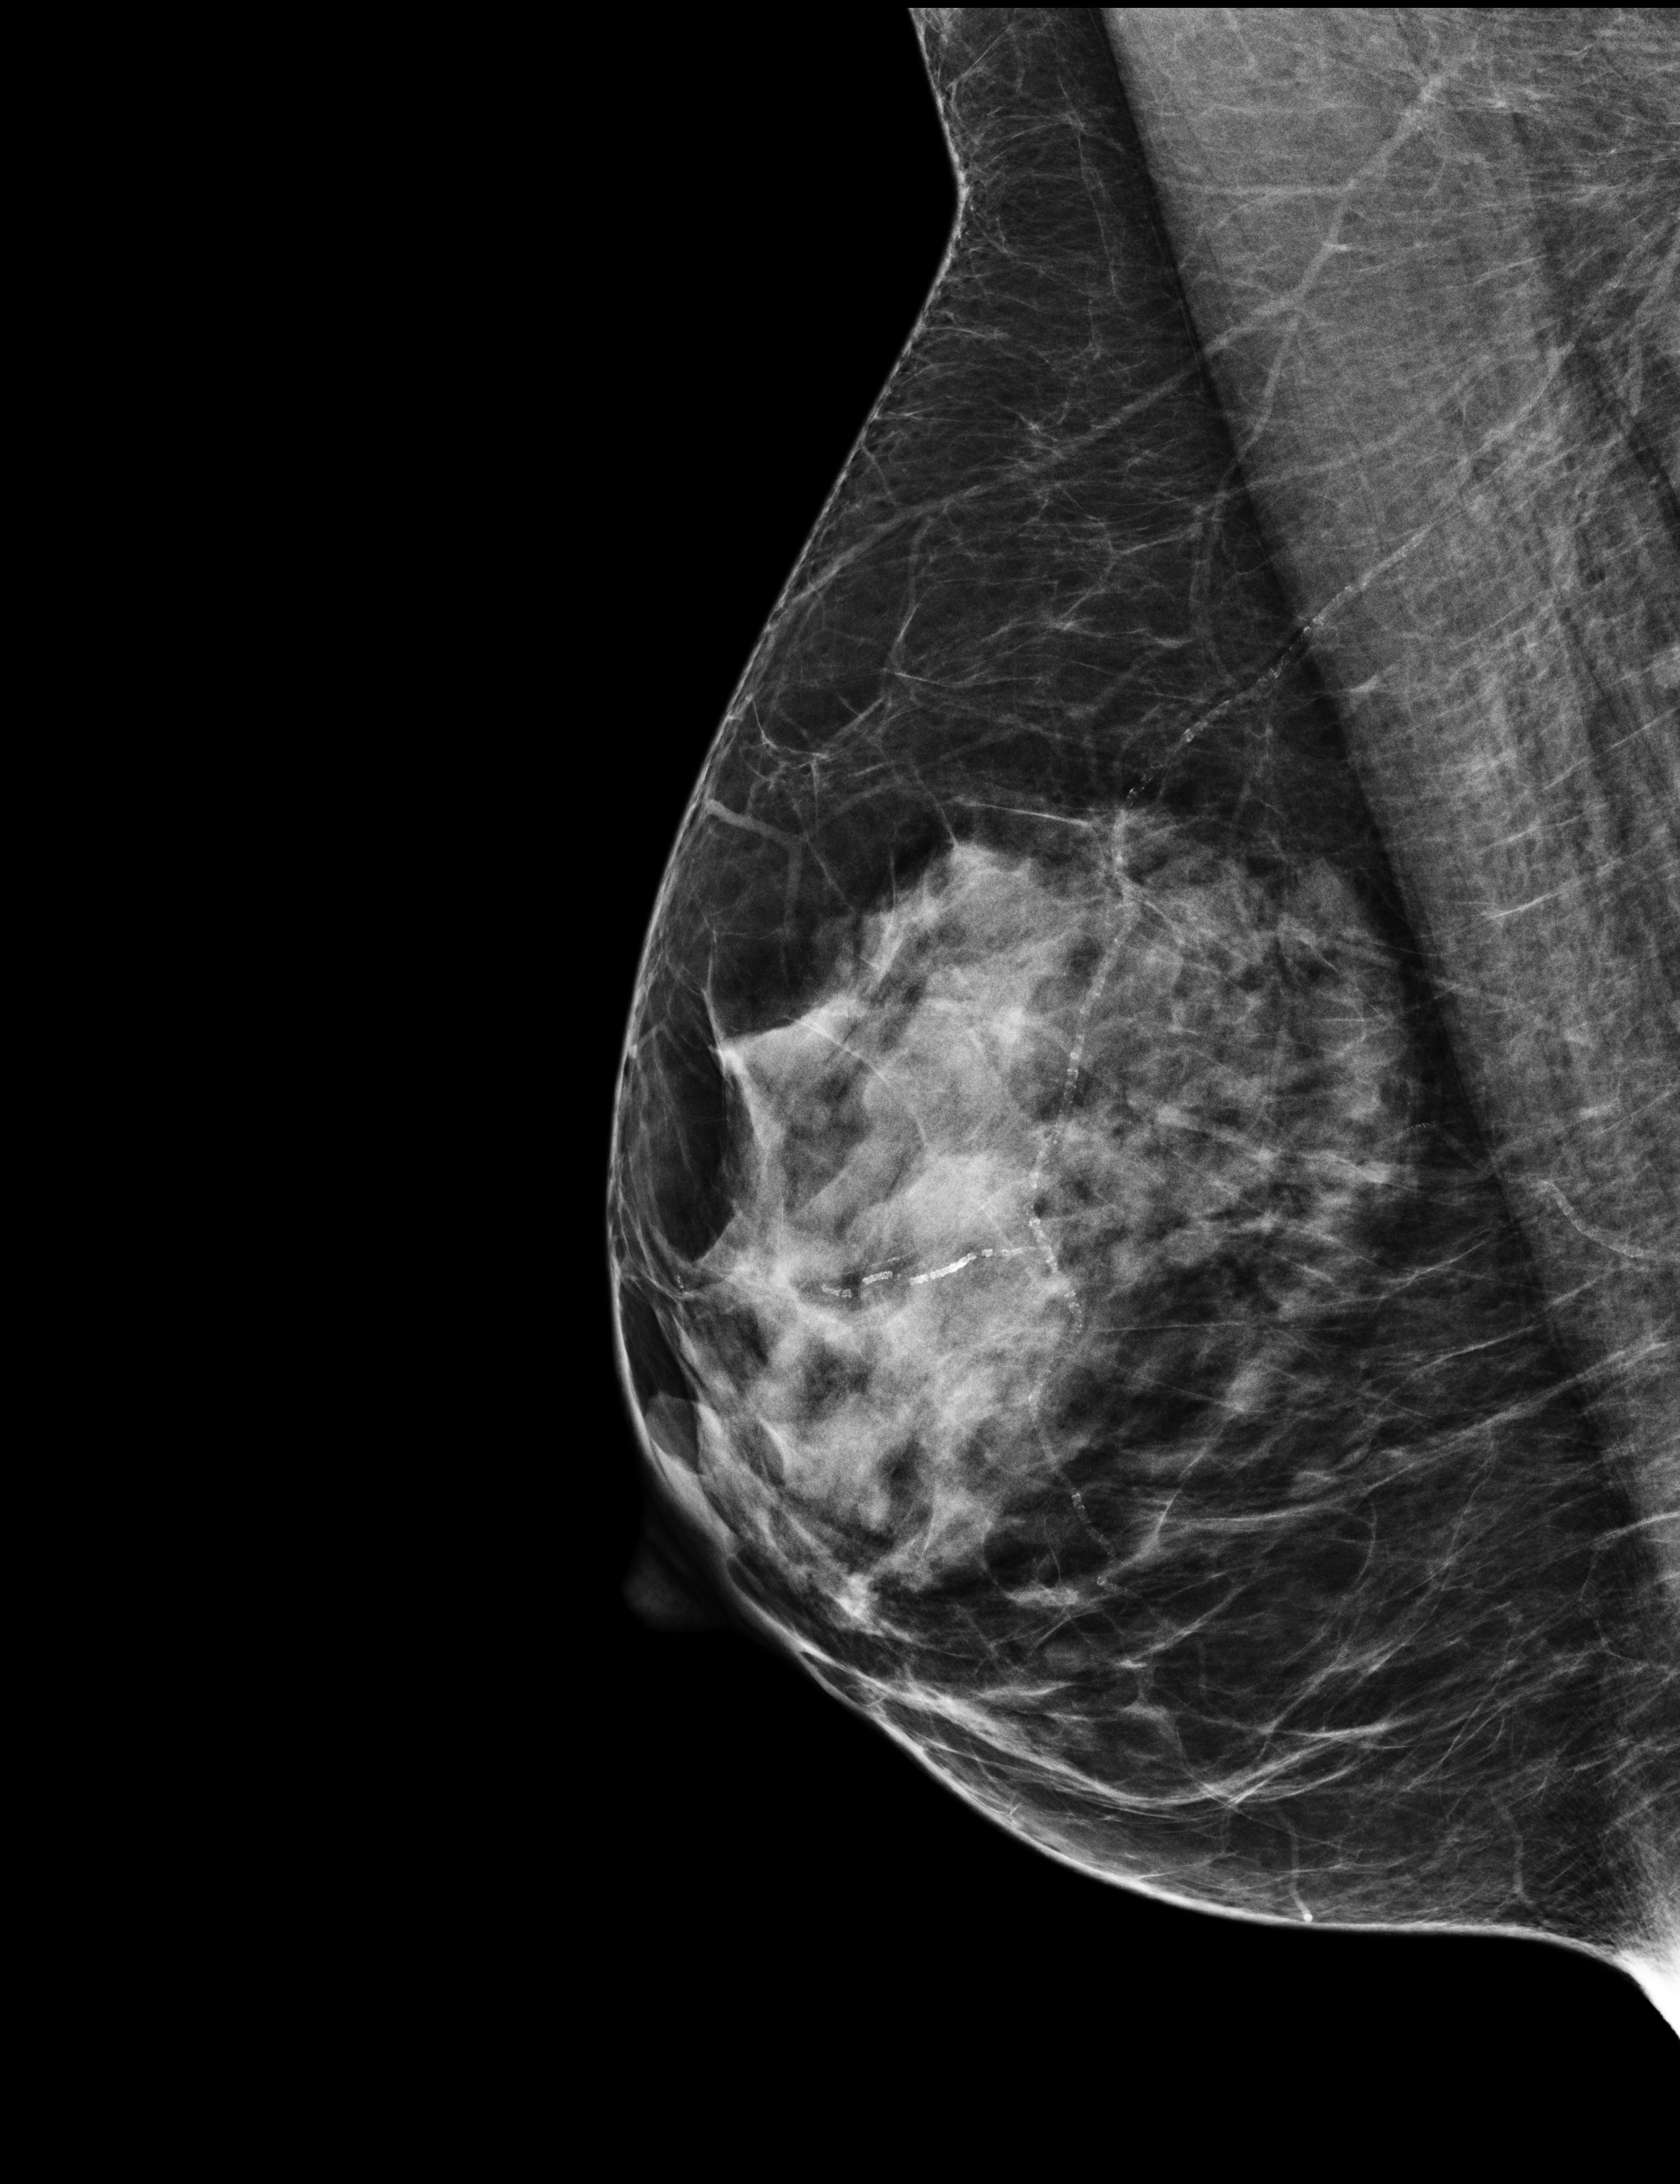
Annual screening mammography examination; compressed breast thickness 44 mm. Female patient, age 58 years.
Image type: full-field digital mammogram. Breast: right. Projection: mediolateral oblique (MLO) view.